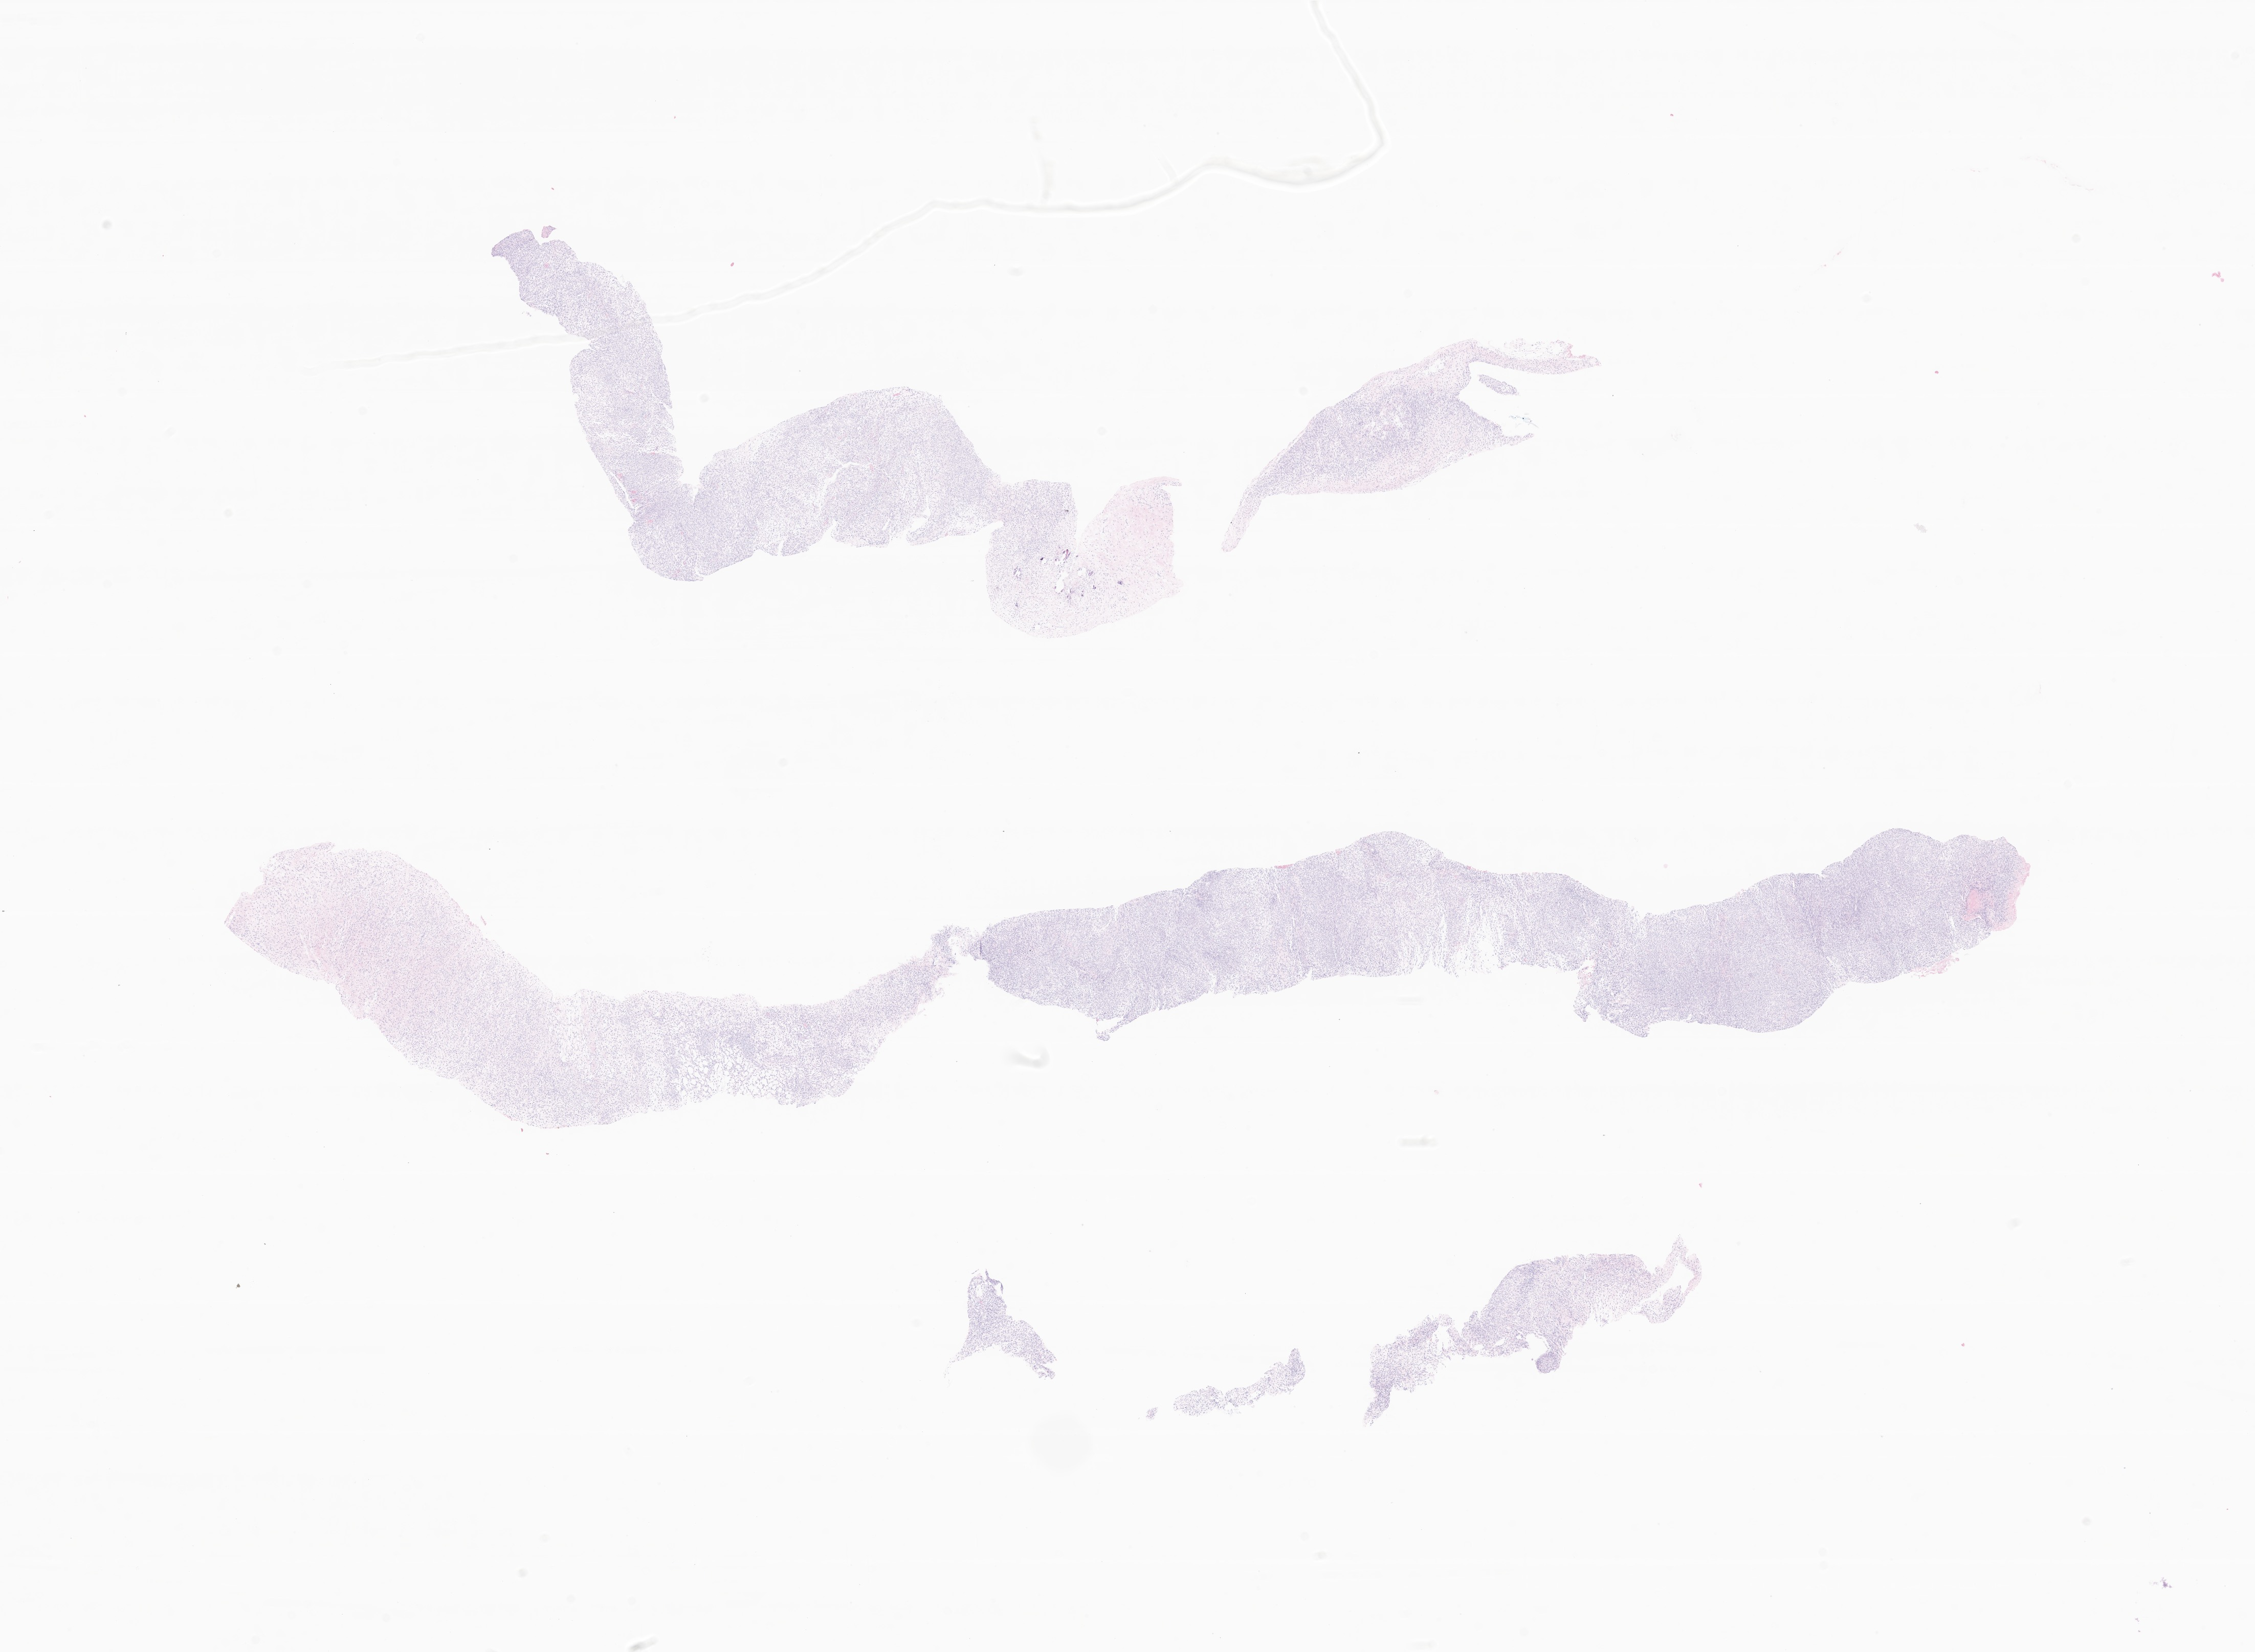
Whole-slide image, haematoxylin and eosin stain of tumor tissue from the soft tissue of lower extremity — a low-resolution overview of the entire scanned area, about 18.6 x 13.6 mm, formalin-fixed, paraffin-embedded (FFPE) tissue. Patient male; age 195 months.
- diagnosis: Synovial sarcoma, spindle cell